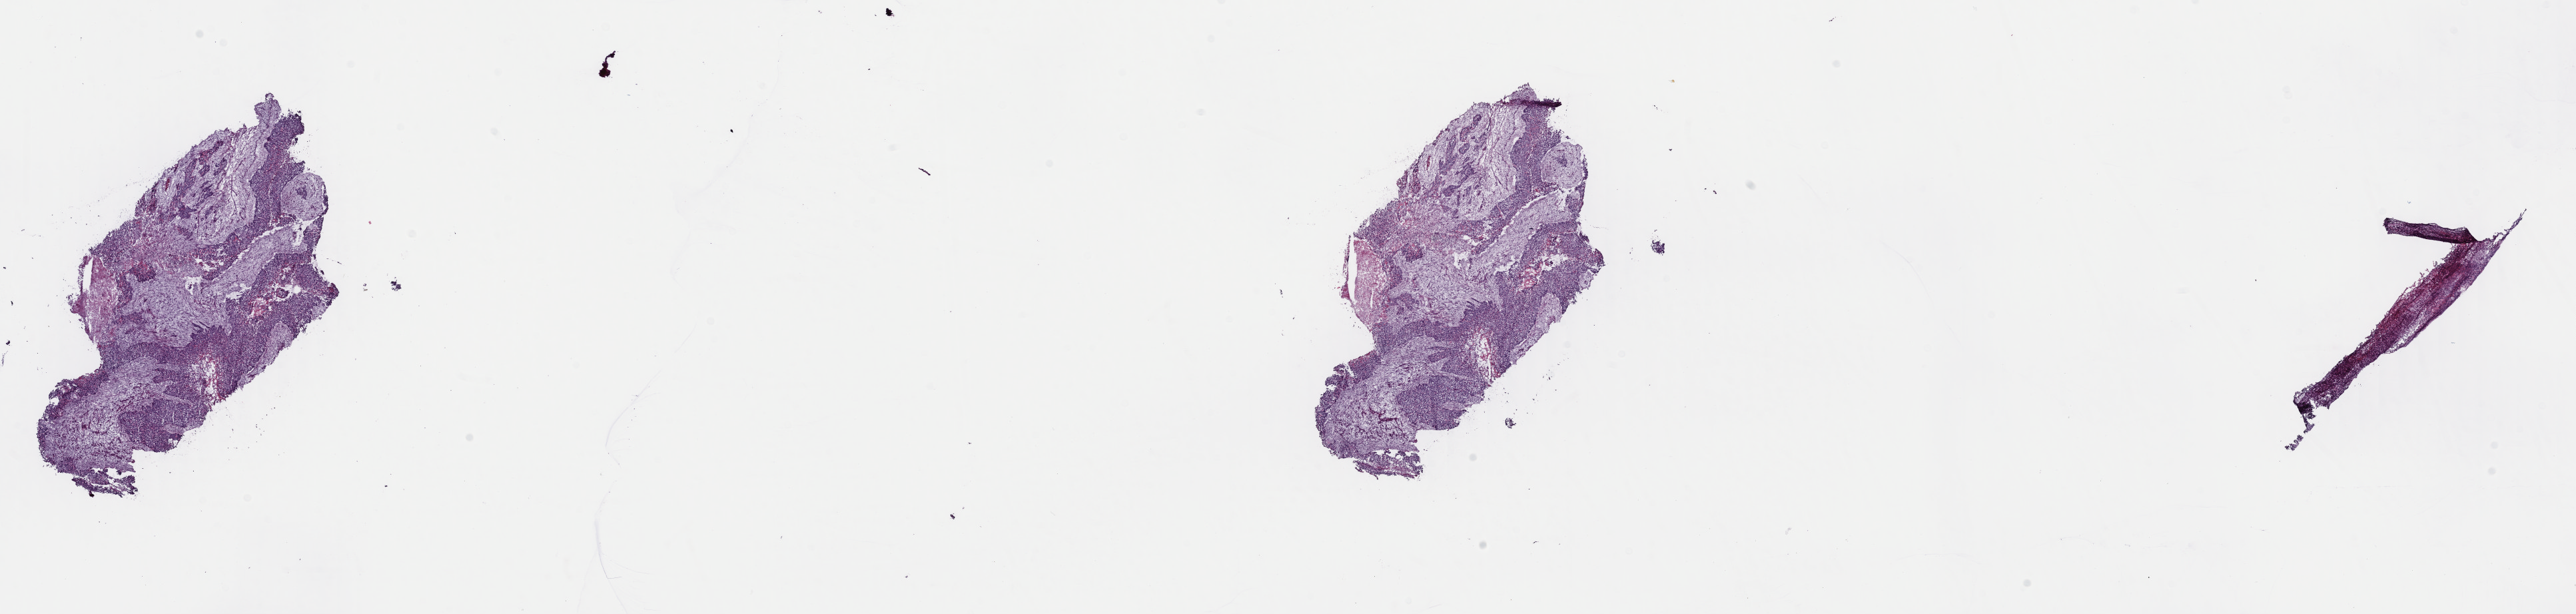
Digitized Hematoxylin and eosin (H&E) stained tissue section (whole slide), shown as a low-resolution overview of the whole scanned area (about 30.5 x 7.3 mm, slide scanned at 40x), frozen section from the top of the tissue portion, lung, primary tumour sample. Male patient; age at initial diagnosis 76 years.
Diagnosis: Squamous cell carcinoma, NOS (upper lobe, lung).